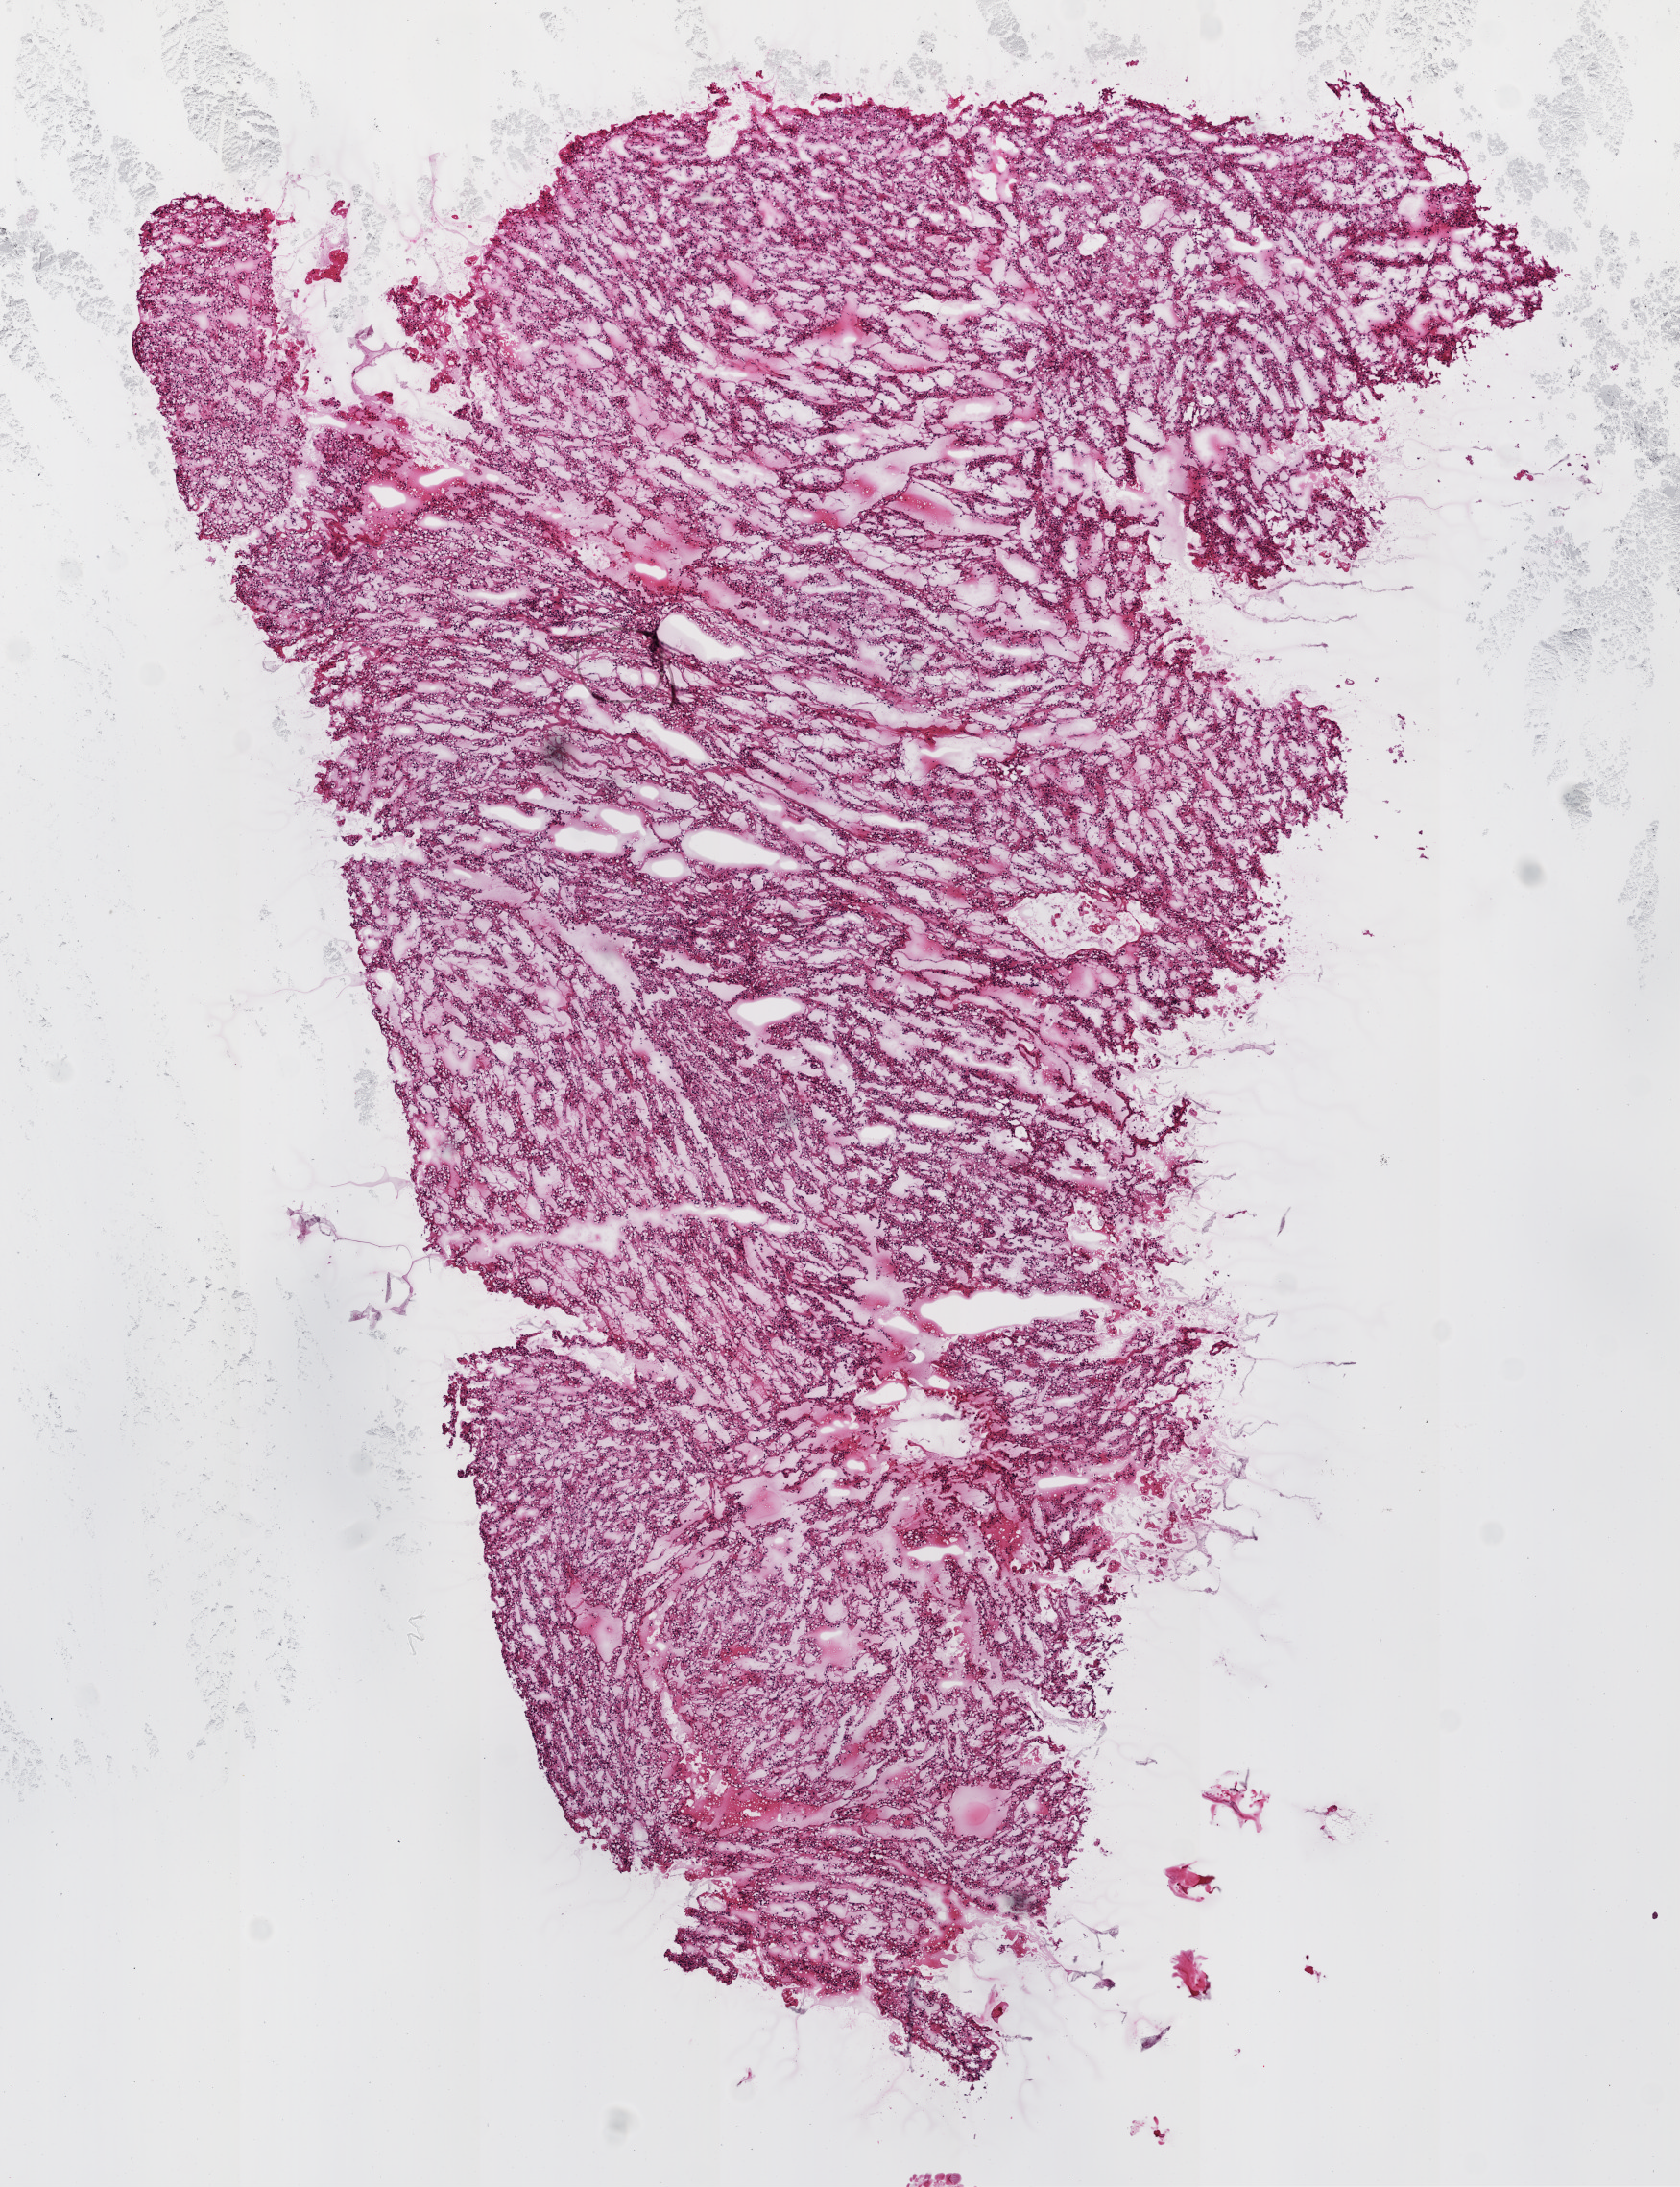
Whole-slide histology image, H&E-stained, whole scanned area (about 7.0 x 9.1 mm) shown as a low-resolution overview. Frozen section from the top of the tissue portion. Sample: primary tumour, kidney. Female, age 80 years at initial diagnosis. Histologic grade: G2 (moderately differentiated). Pathologist review of this section (percent, as recorded): tumour cells 95%, tumour nuclei 85%, normal cells 0%, stromal cells 5%, necrosis 0%.
TNM: T1b NX M0. Pathologic diagnosis: Clear cell adenocarcinoma, NOS. Laterality: left. AJCC pathologic stage: I.